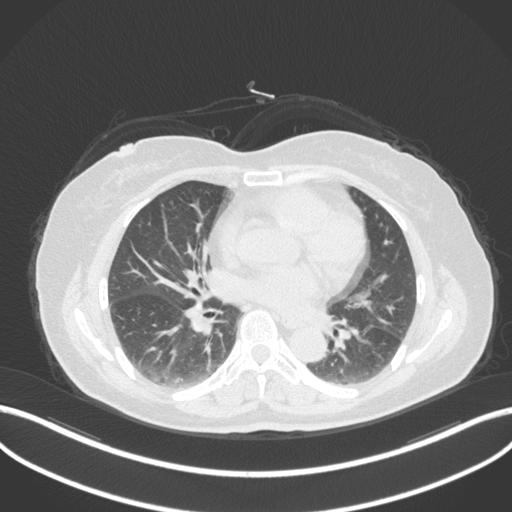
Chest CT, one axial slice; position 178 of 307 along the scan axis; reconstruction kernel B31f; lung window (W 1500 / L -600 HU); 512 × 512 image matrix, field of view 400 × 400 mm. Female patient, age 59 years. Case-level facts recorded for this patient, not image findings: clinical TNM (as recorded): T2a N0 M0.
Structures marked on this image (rectangle marked by the reading radiologist):
- lung tumour (recorded histology: adenocarcinoma): bounding box (x1, y1, x2, y2) in pixels: (351, 327, 374, 351)